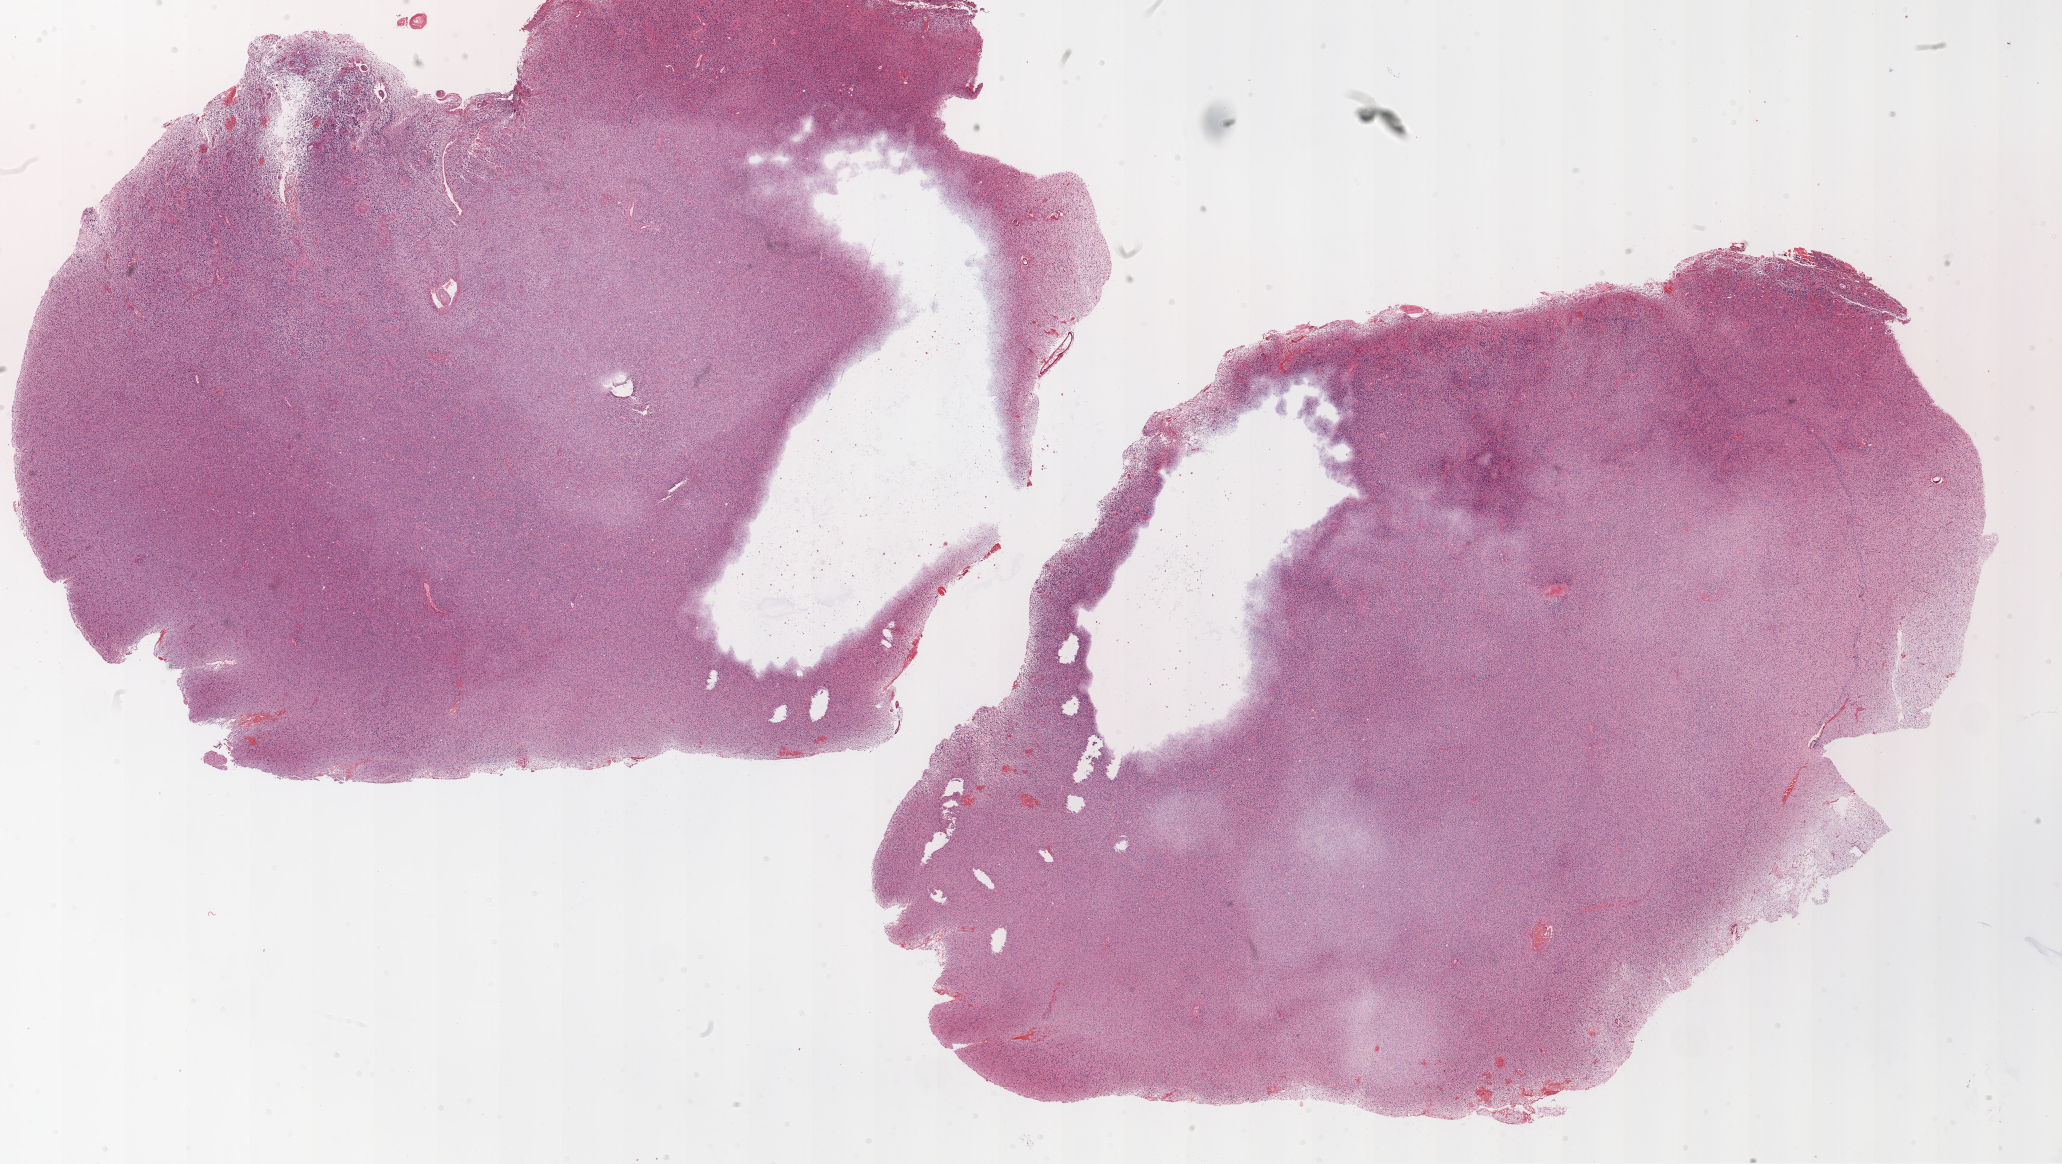
Digitized H&E tissue section (whole slide) — a low-resolution overview of the entire scanned area, about 33.1 x 18.7 mm, FFPE section, brain, primary tumour sample. Male patient; age at initial diagnosis 38 years.
Histologic diagnosis: Glioblastoma.